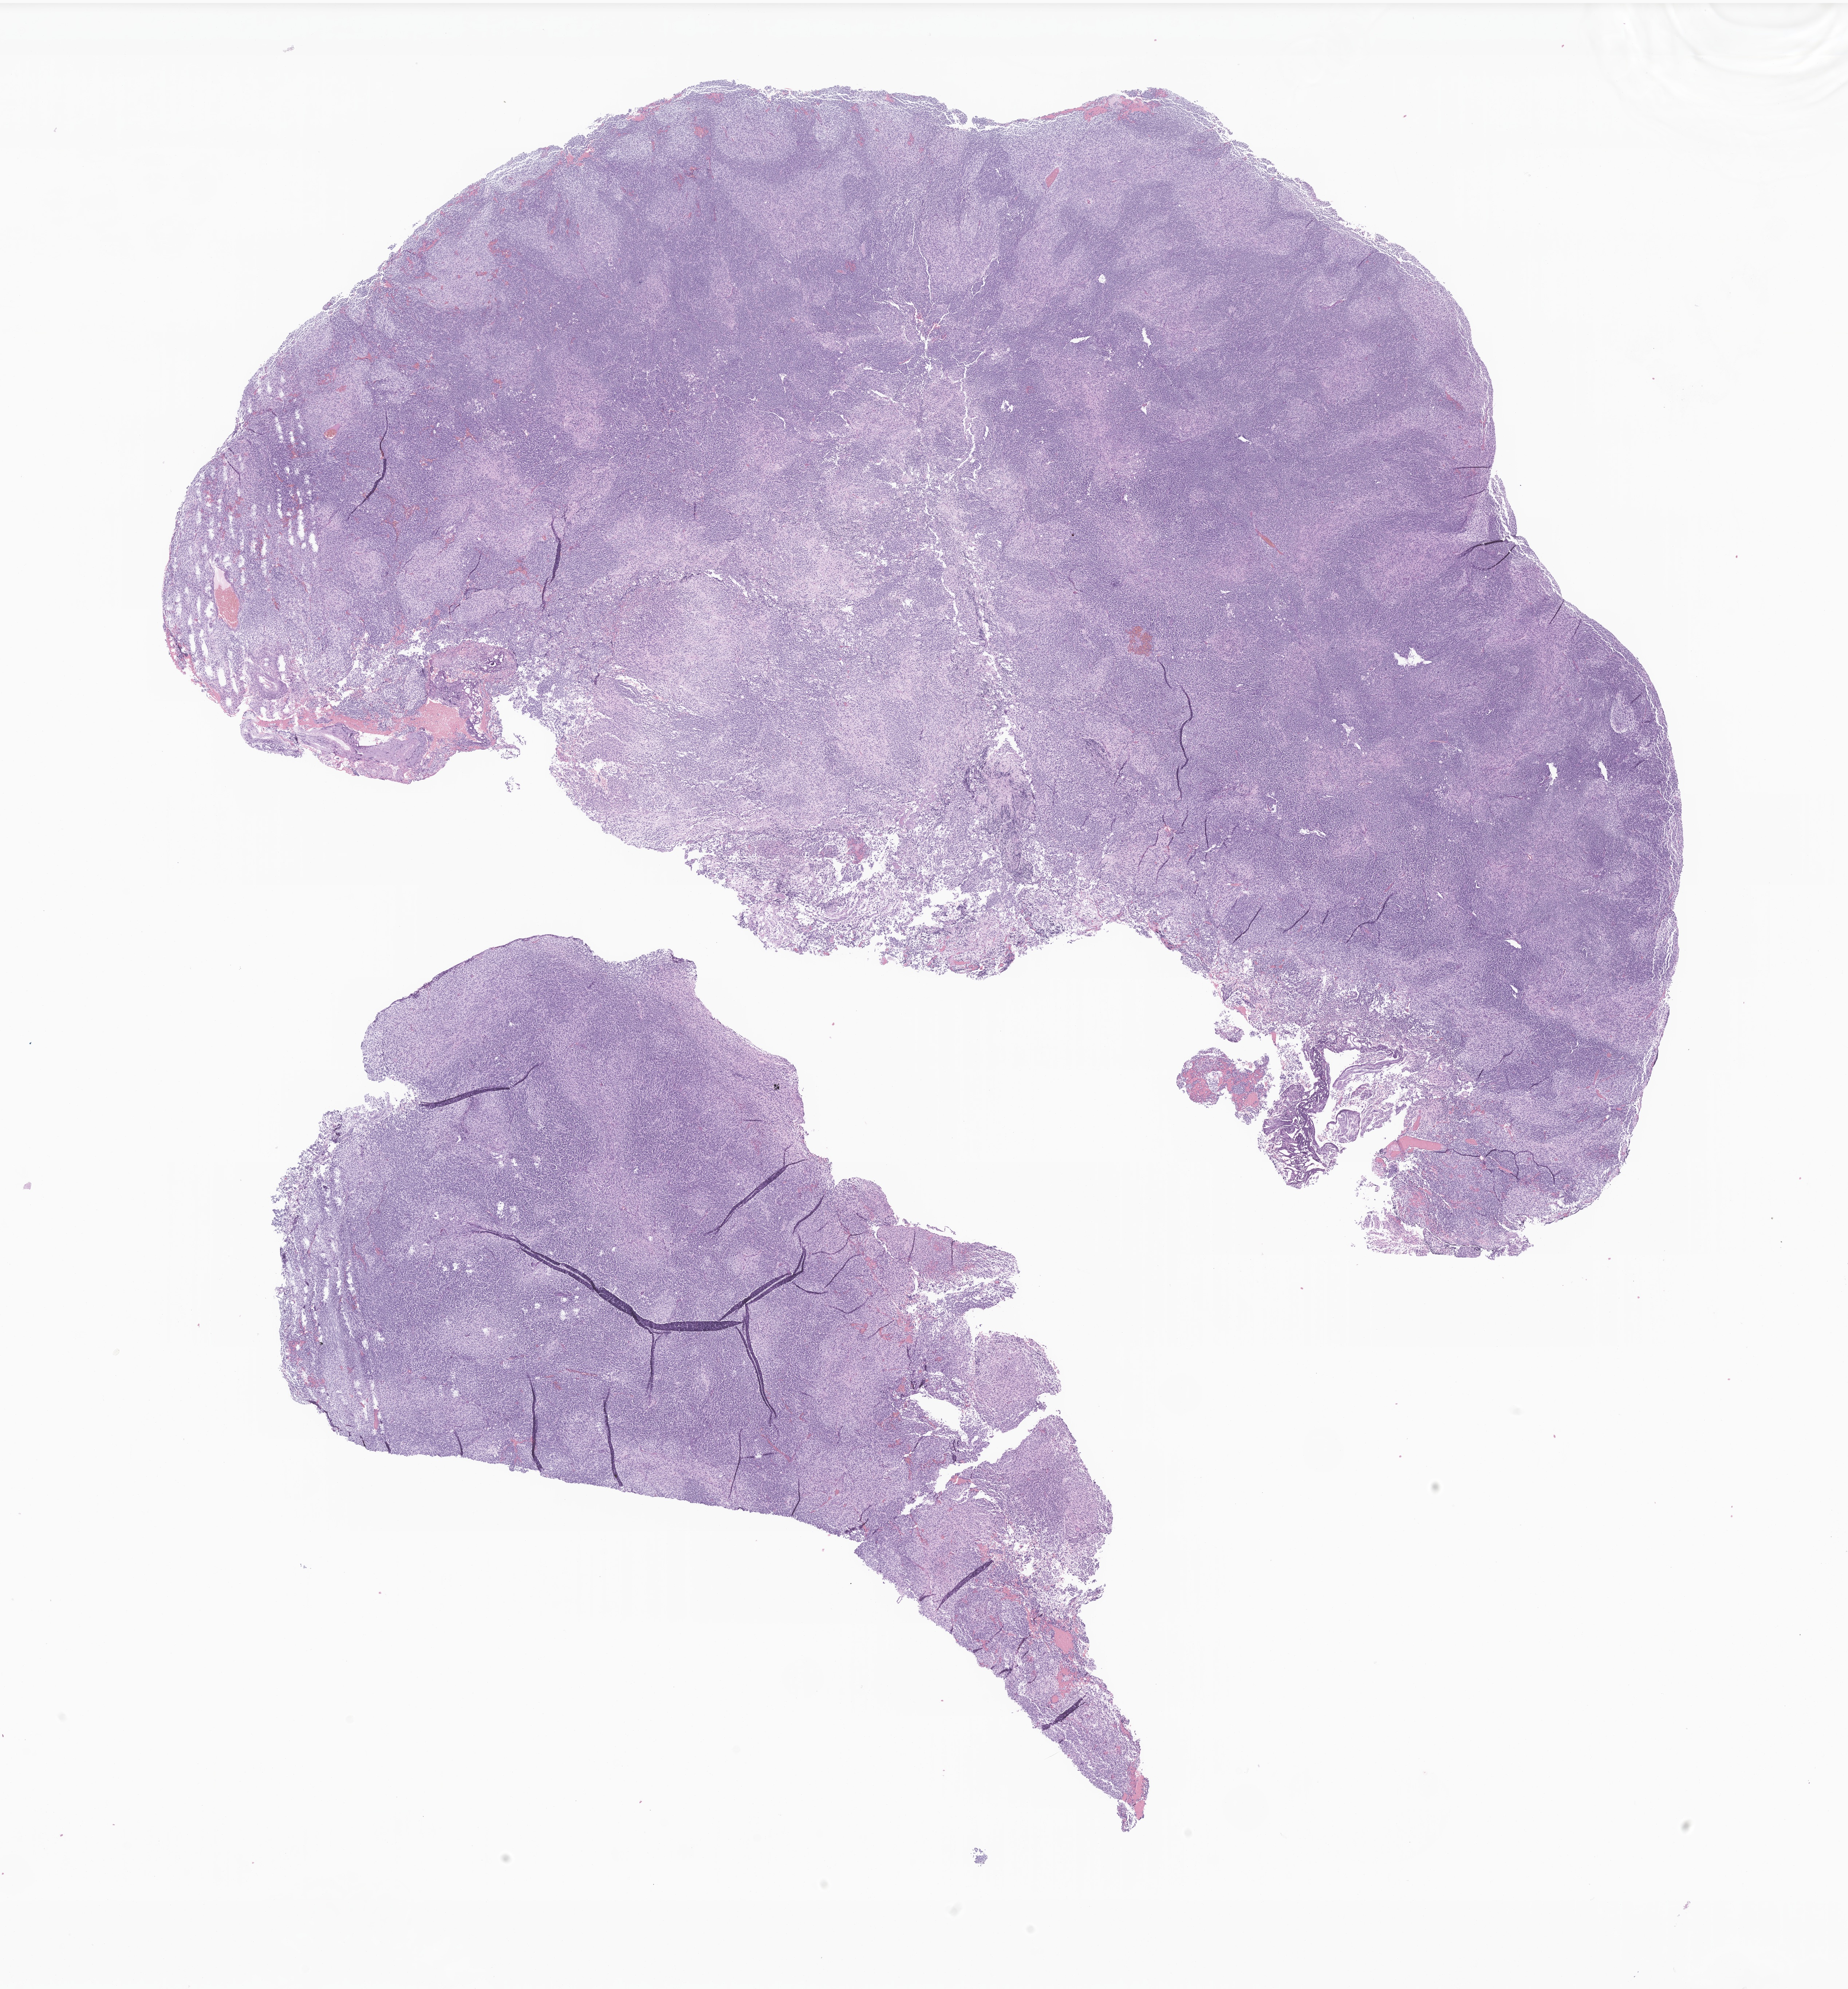
Haematoxylin and eosin whole-slide image of tumor tissue from the brain — a low-resolution overview of the entire scanned area, about 21.4 x 23.0 mm, FFPE section. Patient female; age 79 months (6 years 7 months).
* recorded diagnosis: Medulloblastoma, NOS